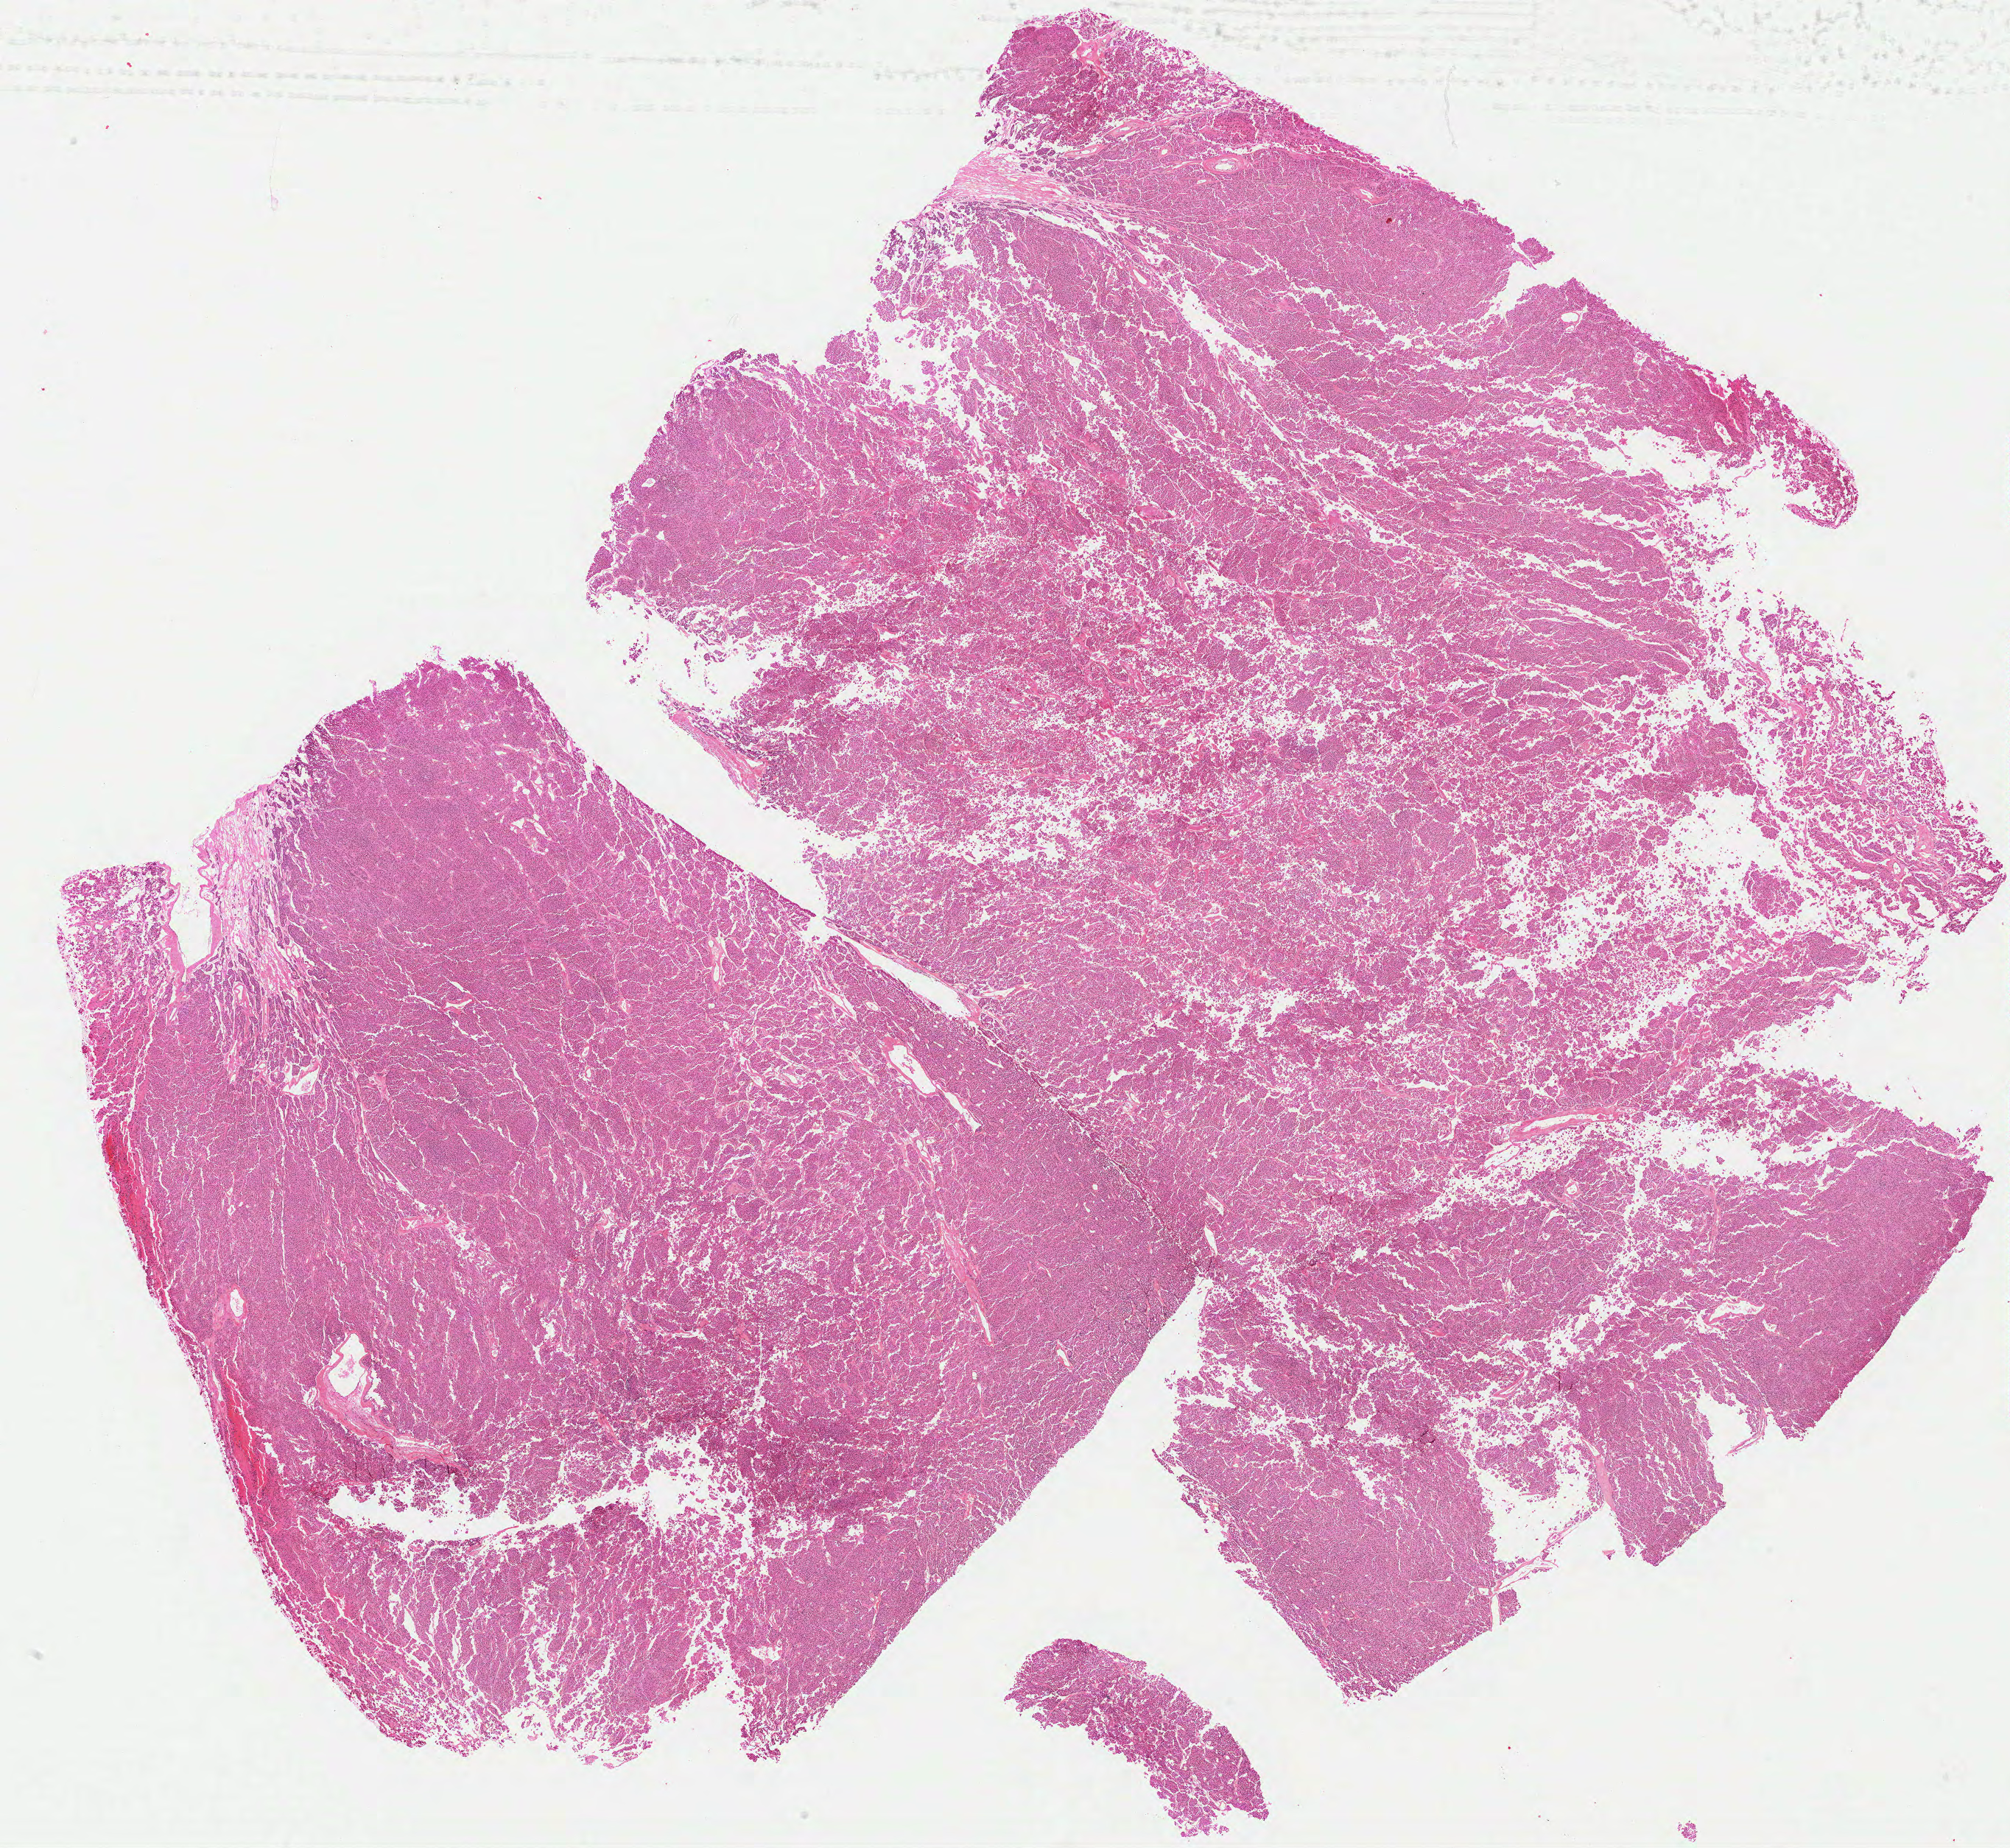
Digitized Hematoxylin and eosin (H&E) stained tissue section (whole slide) — a low-resolution overview of the entire scanned area, about 21.6 x 19.8 mm (slide scanned at 40x); formalin-fixed paraffin-embedded (FFPE) diagnostic section; sample: primary tumour, kidney. Female patient; age at initial diagnosis 48 years. Histologic grade: GX (grade cannot be assessed).
Histologic diagnosis: Clear cell adenocarcinoma, NOS. AJCC pathologic stage: II (6th edition).